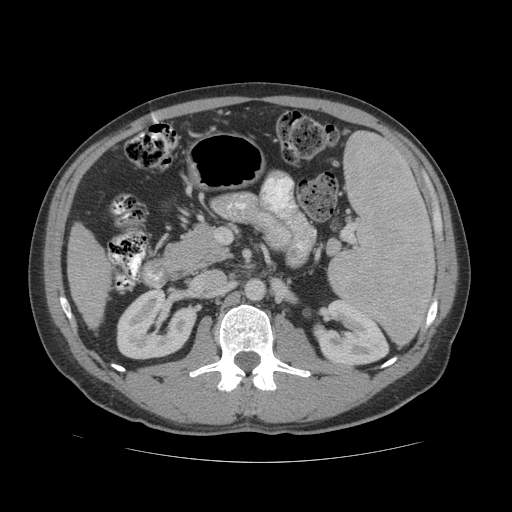
Contrast-enhanced abdominal CT (liver protocol), one axial slice. Slice 16 of 81 in the series (ordered by position). Reconstruction kernel STANDARD. Soft-tissue window (W 400 / L 40 HU). 512 × 512 image matrix, field of view 400 × 400 mm. From the clinical record (not read from this slice): diagnosis: hepatocellular carcinoma (patient treated with transarterial chemoembolisation; whether this scan precedes or follows treatment is not stated here); TNM stage (as recorded): Stage-IVB; Child-Pugh class: B; tumour differentiation: well differentiated; tumour nodularity: multinodular.
Structures marked on this image (semi-automatic segmentation, software-assisted and operator-edited):
- liver parenchyma outside the tumour (the mass and vessels are separate outlines, so this box may not span the whole liver): bounding box [x1, y1, x2, y2] px = [66, 224, 110, 328]